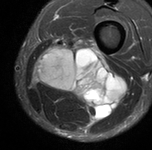
MRI of an extremity soft-tissue mass, one axial slice; position 33 of 90 along the scan axis; STIR; MR volume resampled by the dataset authors to the PET/CT grid (not the native acquisition matrix); 3.27 mm slice thickness; 152 × 150 image matrix, field of view 148 × 146 mm. Male patient. Case-level facts recorded for this patient, not image findings: histological type: undifferentiated pleomorphic liposarcoma; grade: high; site of the primary tumour: left thigh.
Outlined on this slice (expert contour drawn on MRI and transferred to this co-registered scan by the dataset authors):
- gross tumour volume including surrounding oedema: box from (x=34, y=39) to (x=122, y=122) px
- gross tumour volume (mass): (x=43, y=55)–(x=115, y=108)